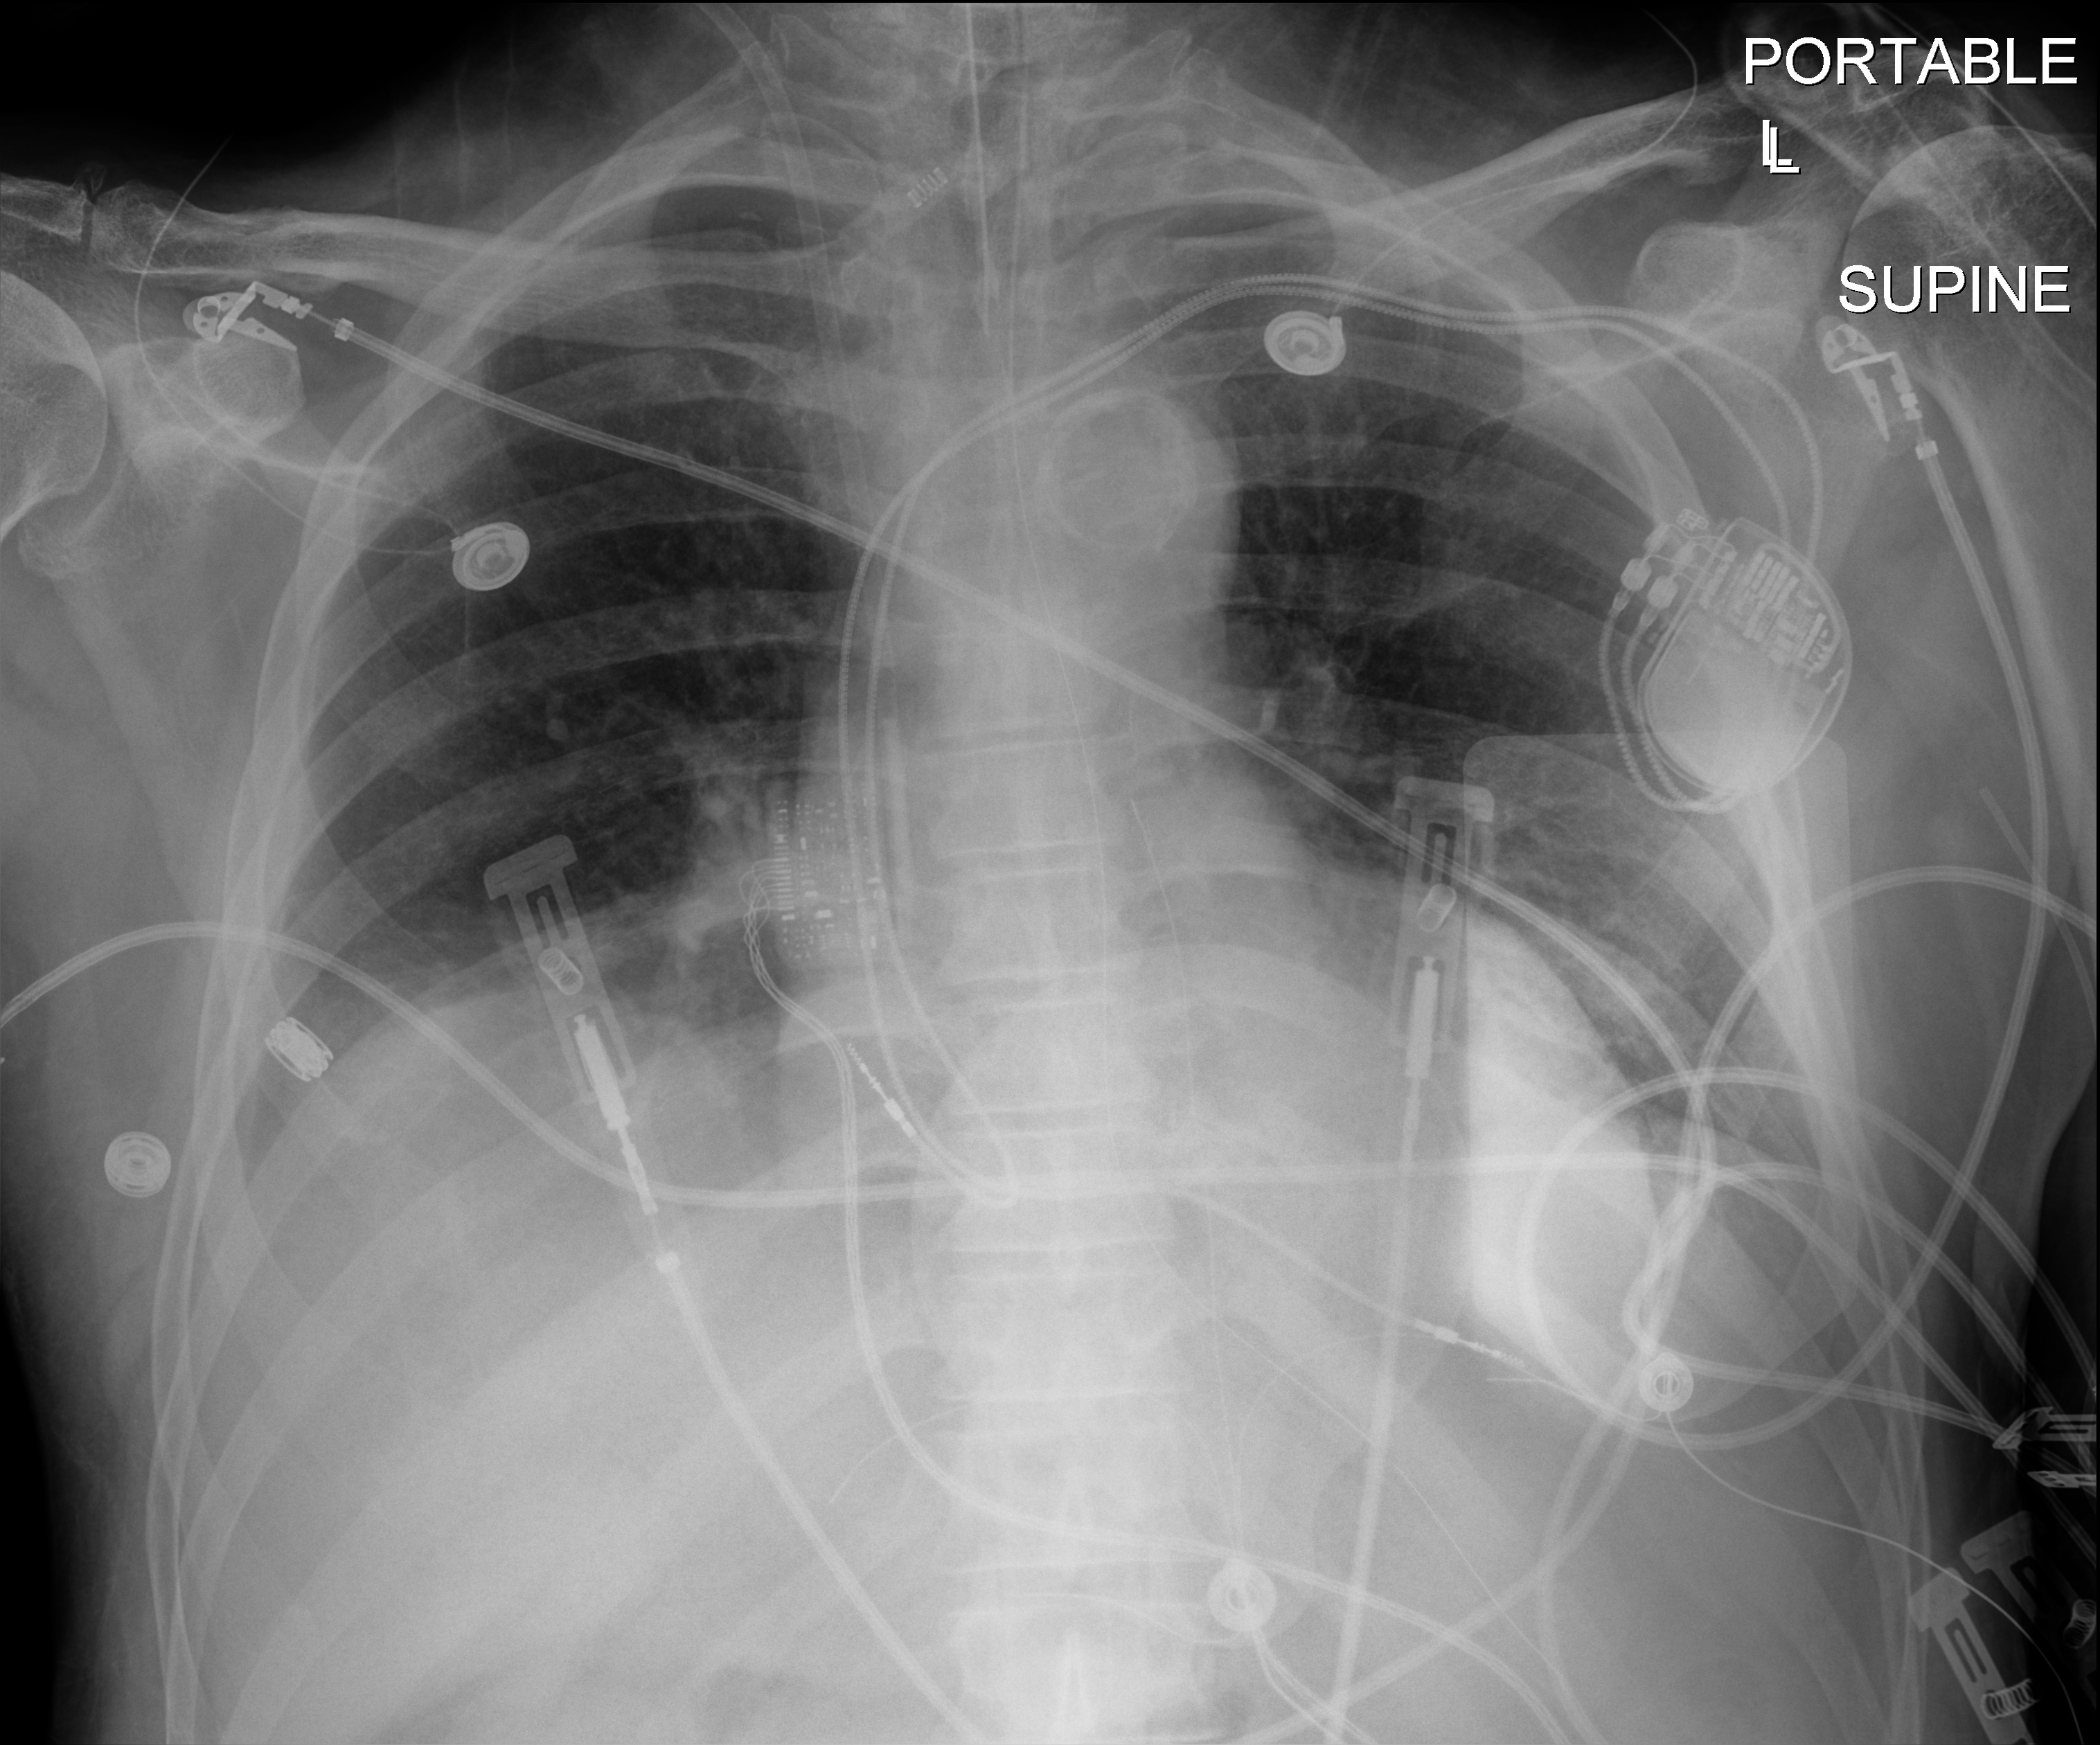
Bedside chest radiograph (digital radiography), anteroposterior (AP) projection. Male patient hospitalised with COVID-19, age 60–74 years.
From the hospital-stay record, not from the radiograph (when in the stay this image was taken is not recorded):
- admitted to intensive care during this hospital stay: yes